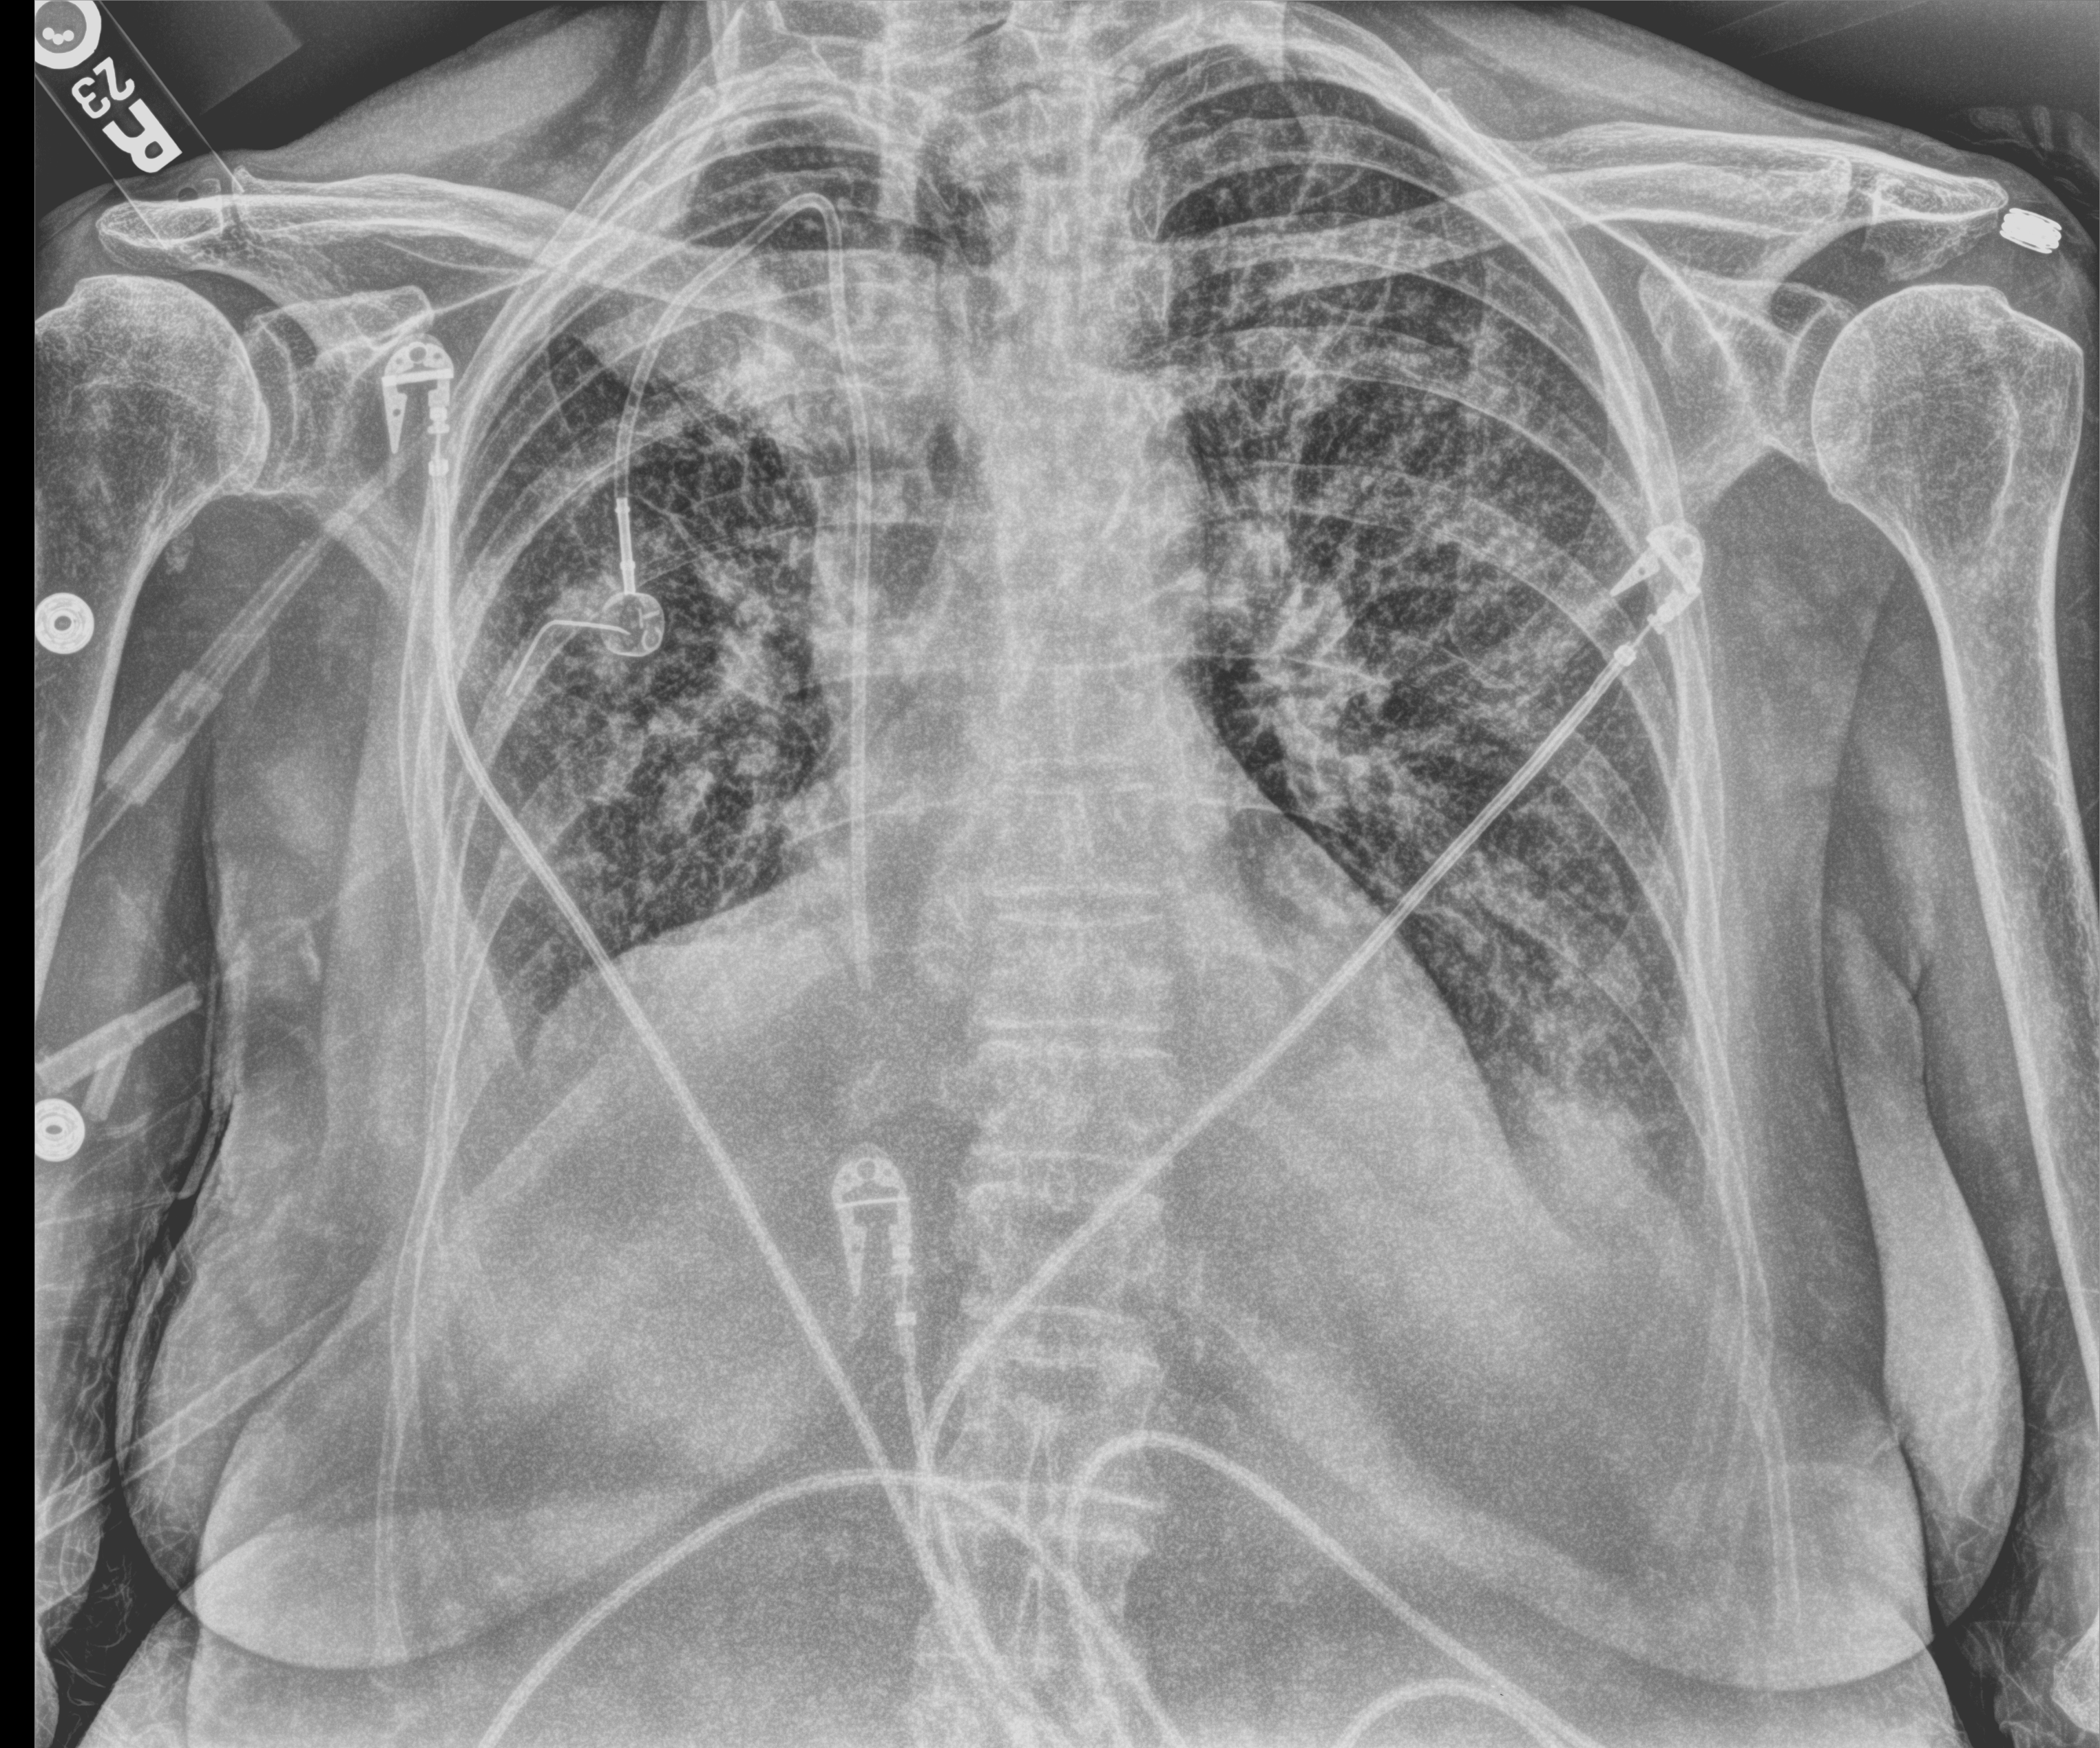
Bedside chest radiograph (computed radiography); anteroposterior (AP) projection. Female patient hospitalised with COVID-19, age 60–74 years.
From the hospital-stay record, not from the radiograph (when in the stay this image was taken is not recorded): mechanically ventilated during this hospital stay: no; admitted to intensive care during this hospital stay: no.